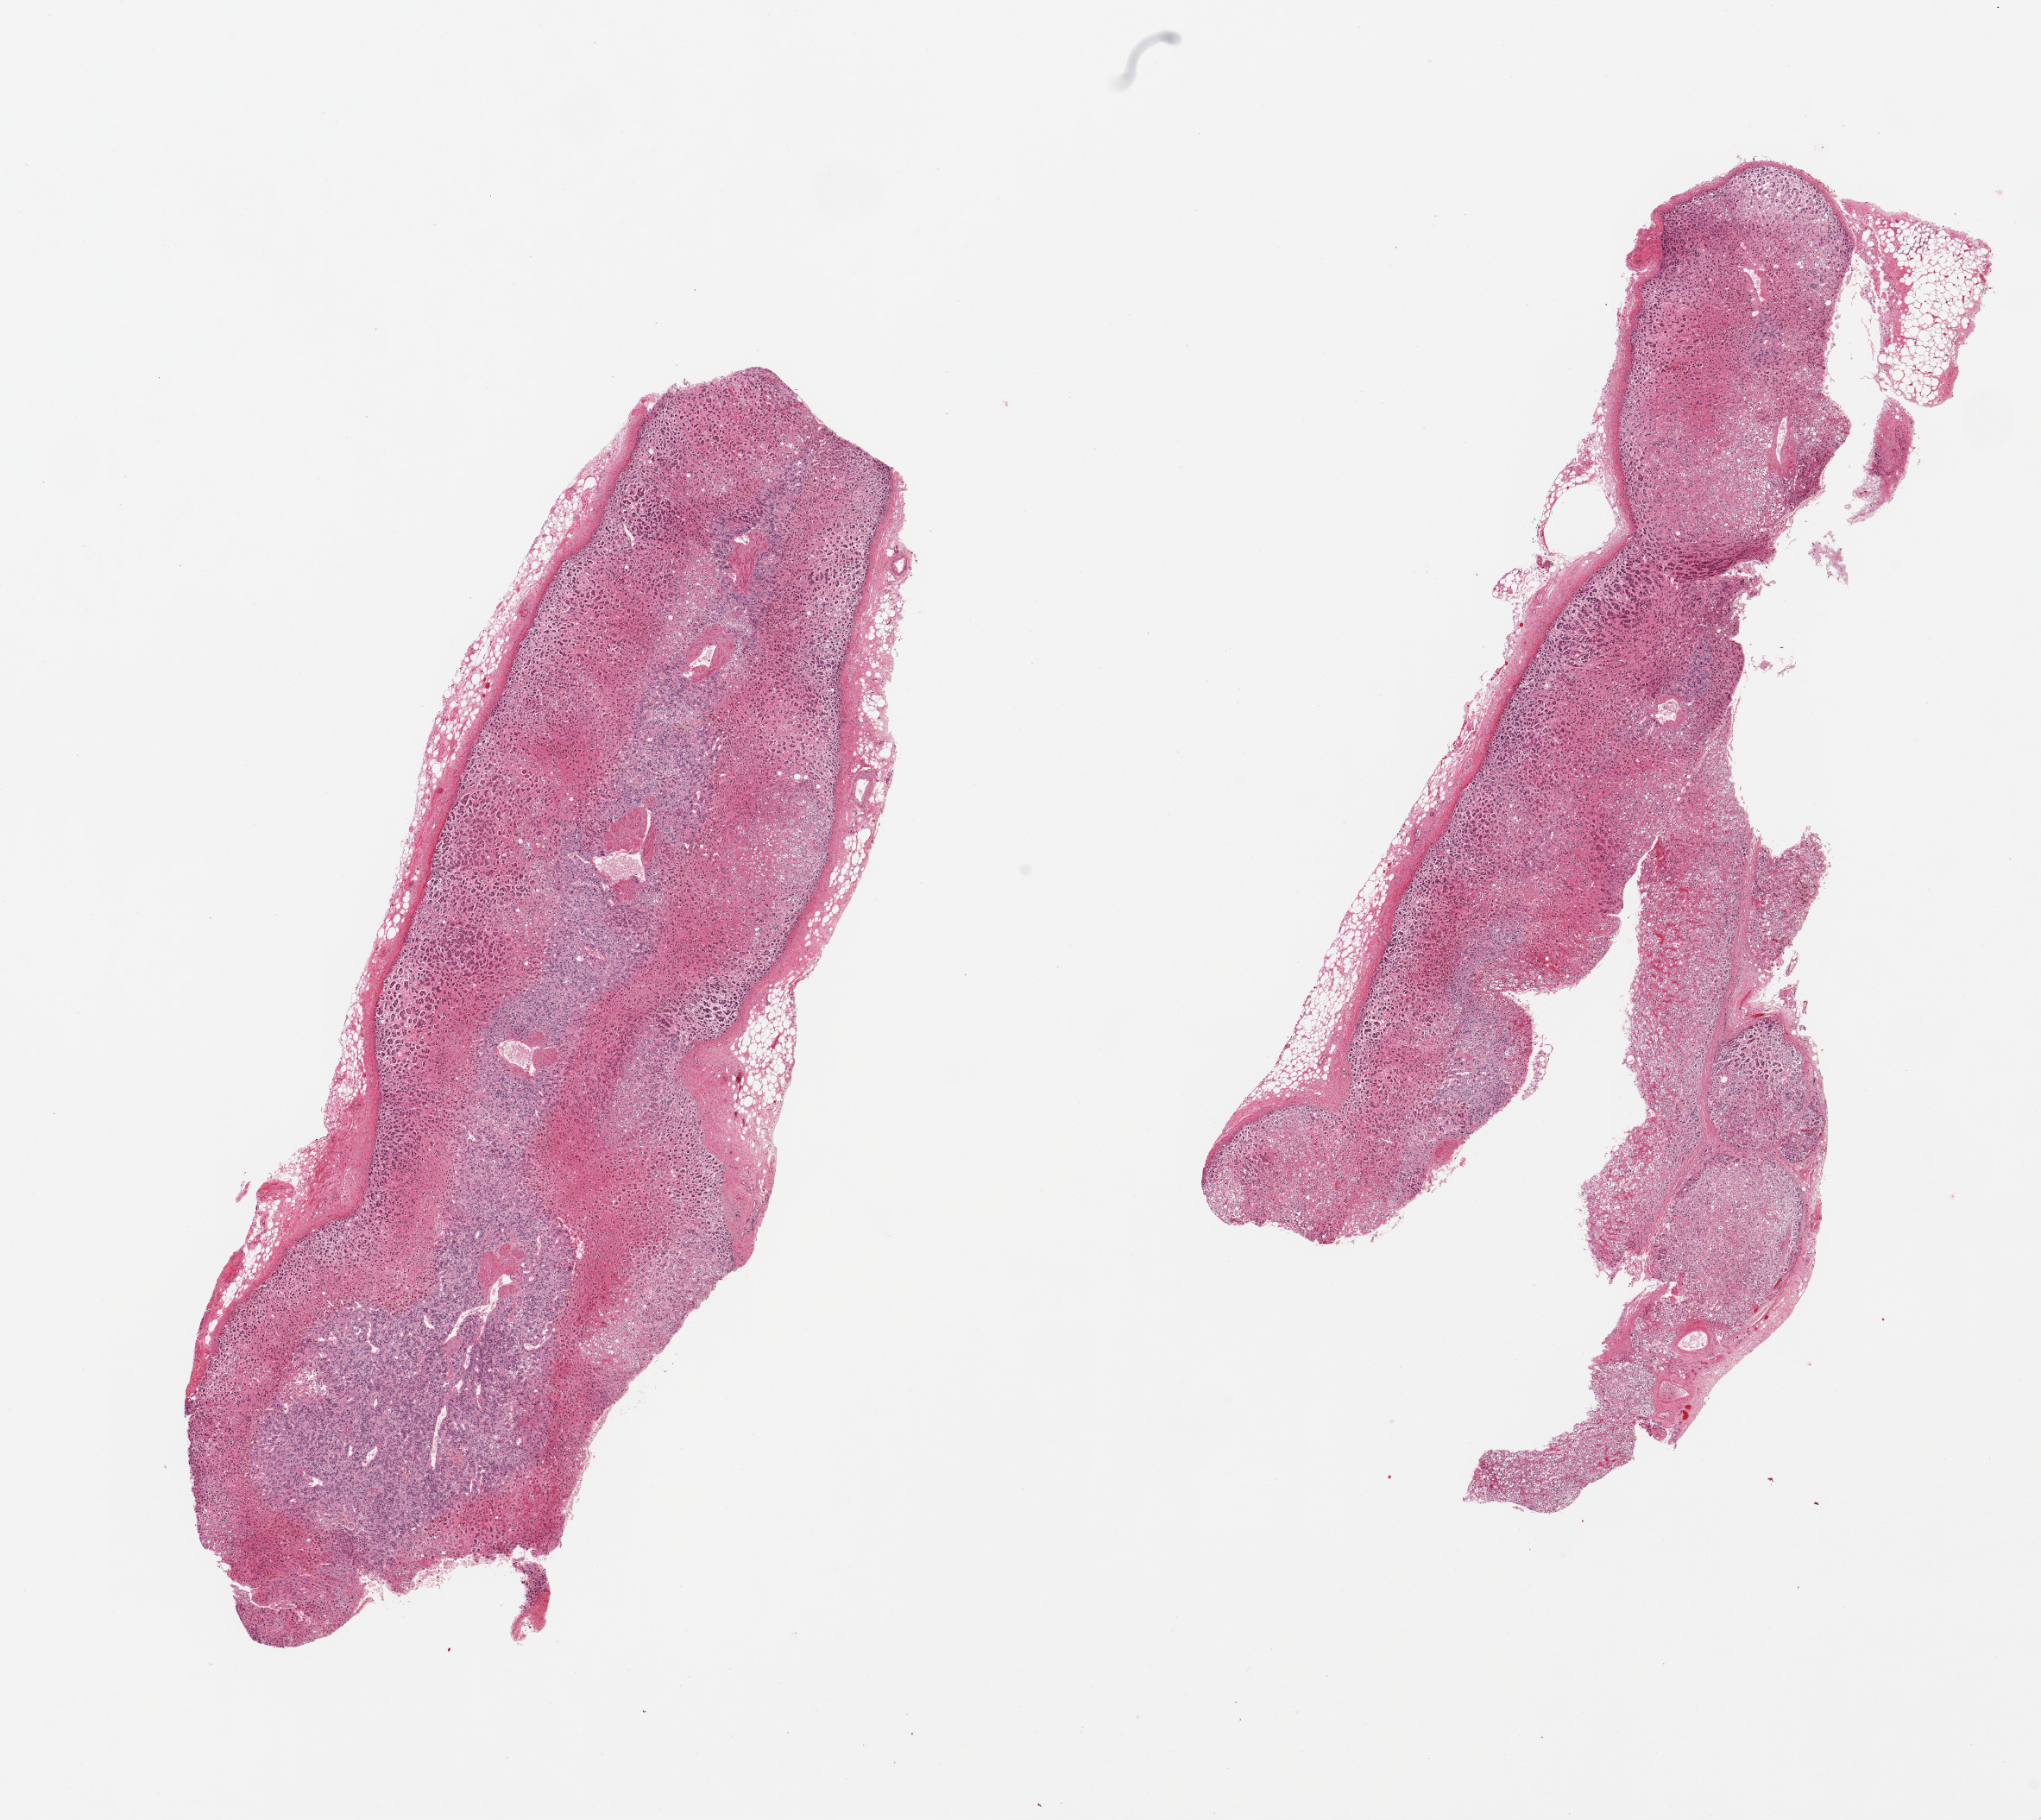
Whole-slide image, H&E stain, brightfield — shown as a low-resolution overview of the whole scanned area (about 18.7 x 16.7 mm); PAXgene-fixed, paraffin-embedded tissue; section of adrenal gland (target tissue); donor tissue sample. Donor sex: male.
* review note (as recorded): 2 pieces; well dissected with <10% external fat